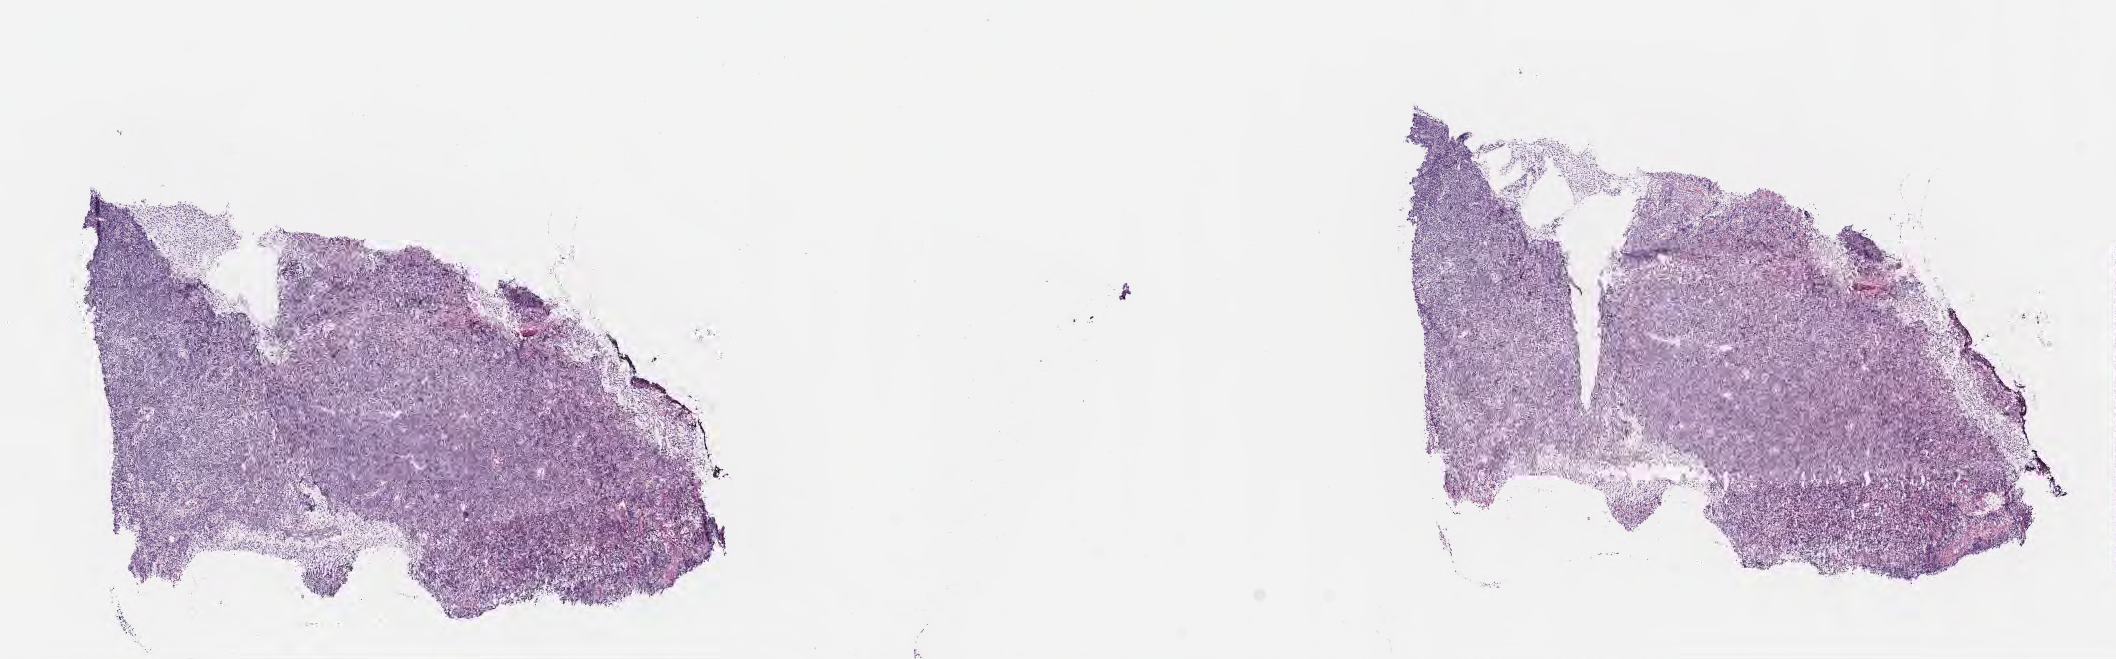
Digitized haematoxylin and eosin-stained section, a low-resolution overview of the entire scanned area, about 17.1 x 5.3 mm. Cryosection. Primary tumor. Site: cranium. Patient: female, age at initial diagnosis 7 years. Pathologist review of this section (percent, as recorded): tumor cells 90%, tumor nuclei 95%, stromal cells 5%, necrosis 5%, normal cells 0%. Infiltration values recorded for this section: lymphocyte infiltration 60%, monocyte infiltration 20%, neutrophil infiltration 5%.
* section: top of the tissue portion
* Ann Arbor stage (patient): Stage IV
* diagnosis: Burkitt lymphoma, NOS